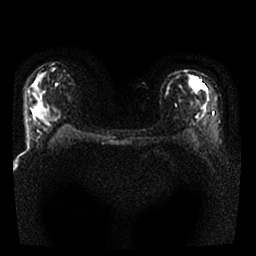
Breast MRI, one axial slice. Slice 14 of 25 in the series (ordered by position). Diffusion-weighted series; image 2 of 4 stored at this slice position (different b-values; order by instance number). 1.5 T. 4 mm slice thickness. 256 × 256 image matrix, field of view 310 × 310 mm. Female patient.
Annotated regions visible in this slice (outlined manually by an expert reader):
- tumour on diffusion-weighted imaging: bounding box [x1, y1, x2, y2] px = [191, 78, 202, 91]